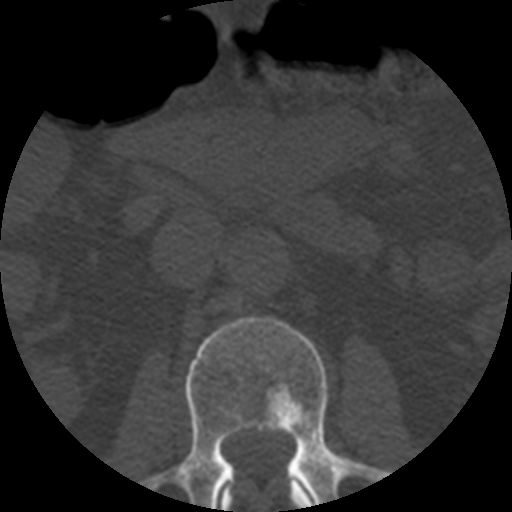
CT including the spine, one axial slice; slice 158 of 508 in the series (ordered by position); reconstruction kernel STANDARD; bone window (W 1800 / L 400 HU); 1.25 mm slice thickness; 512 × 512 image matrix, field of view 160 × 160 mm. Patient age 57 years. Case-level facts recorded for this patient, not image findings: primary cancer: prostate.
Annotated regions visible in this slice (semi-automatically segmented with operator editing):
- L1 vertebra: bounding box (x1, y1, x2, y2) in pixels: (219, 482, 314, 512)
- L2 vertebra: (141, 317, 389, 512)